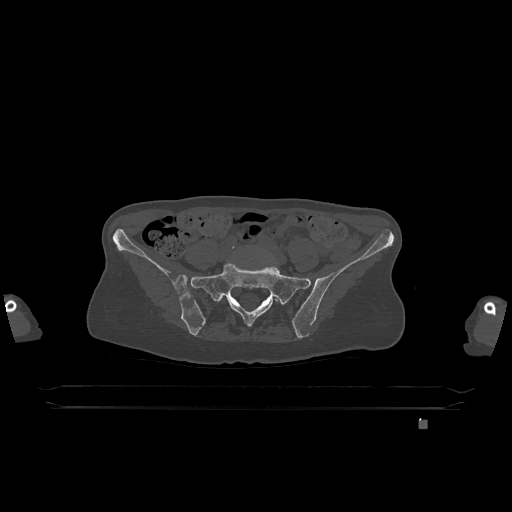
CT including the spine, one axial slice. Position 197 of 1317 along the scan axis. Bone window (W 1800 / L 400 HU). 512 × 512 image matrix. Patient: female, 74 years. From the clinical record (not read from this slice): primary cancer: lung; vertebrae with lytic lesions (as recorded): T1, T4, T5, T6, L4, L5.
Structures marked on this image (semi-automatic segmentation, software-assisted and operator-edited):
- L5 vertebra: bounding box [x1, y1, x2, y2] px = [221, 298, 278, 302]